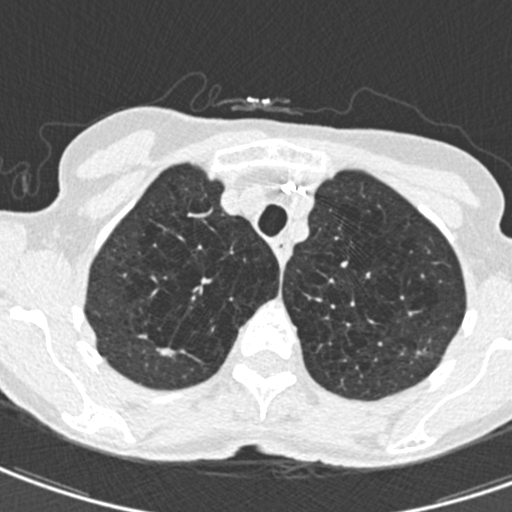
Axial slice from a low-dose chest CT screening exam. Second screening round (one year after baseline). Lung window (W 1500 / L -600 HU). 0.75 mm slice thickness. 120 kVp. Slice 103 of 498 in the series. 512 × 512 image matrix, field of view 272 × 272 mm. Female participant, aged 71 years at enrolment. Current smoker at enrolment.
Expert reader's lesion annotation, box from (x=405, y=332) to (x=444, y=371) px. The screening reader recorded 2 non-calcified nodules or masses ≥4 mm on this exam (right upper lobe, left upper lobe); which of them this box marks is not recorded.